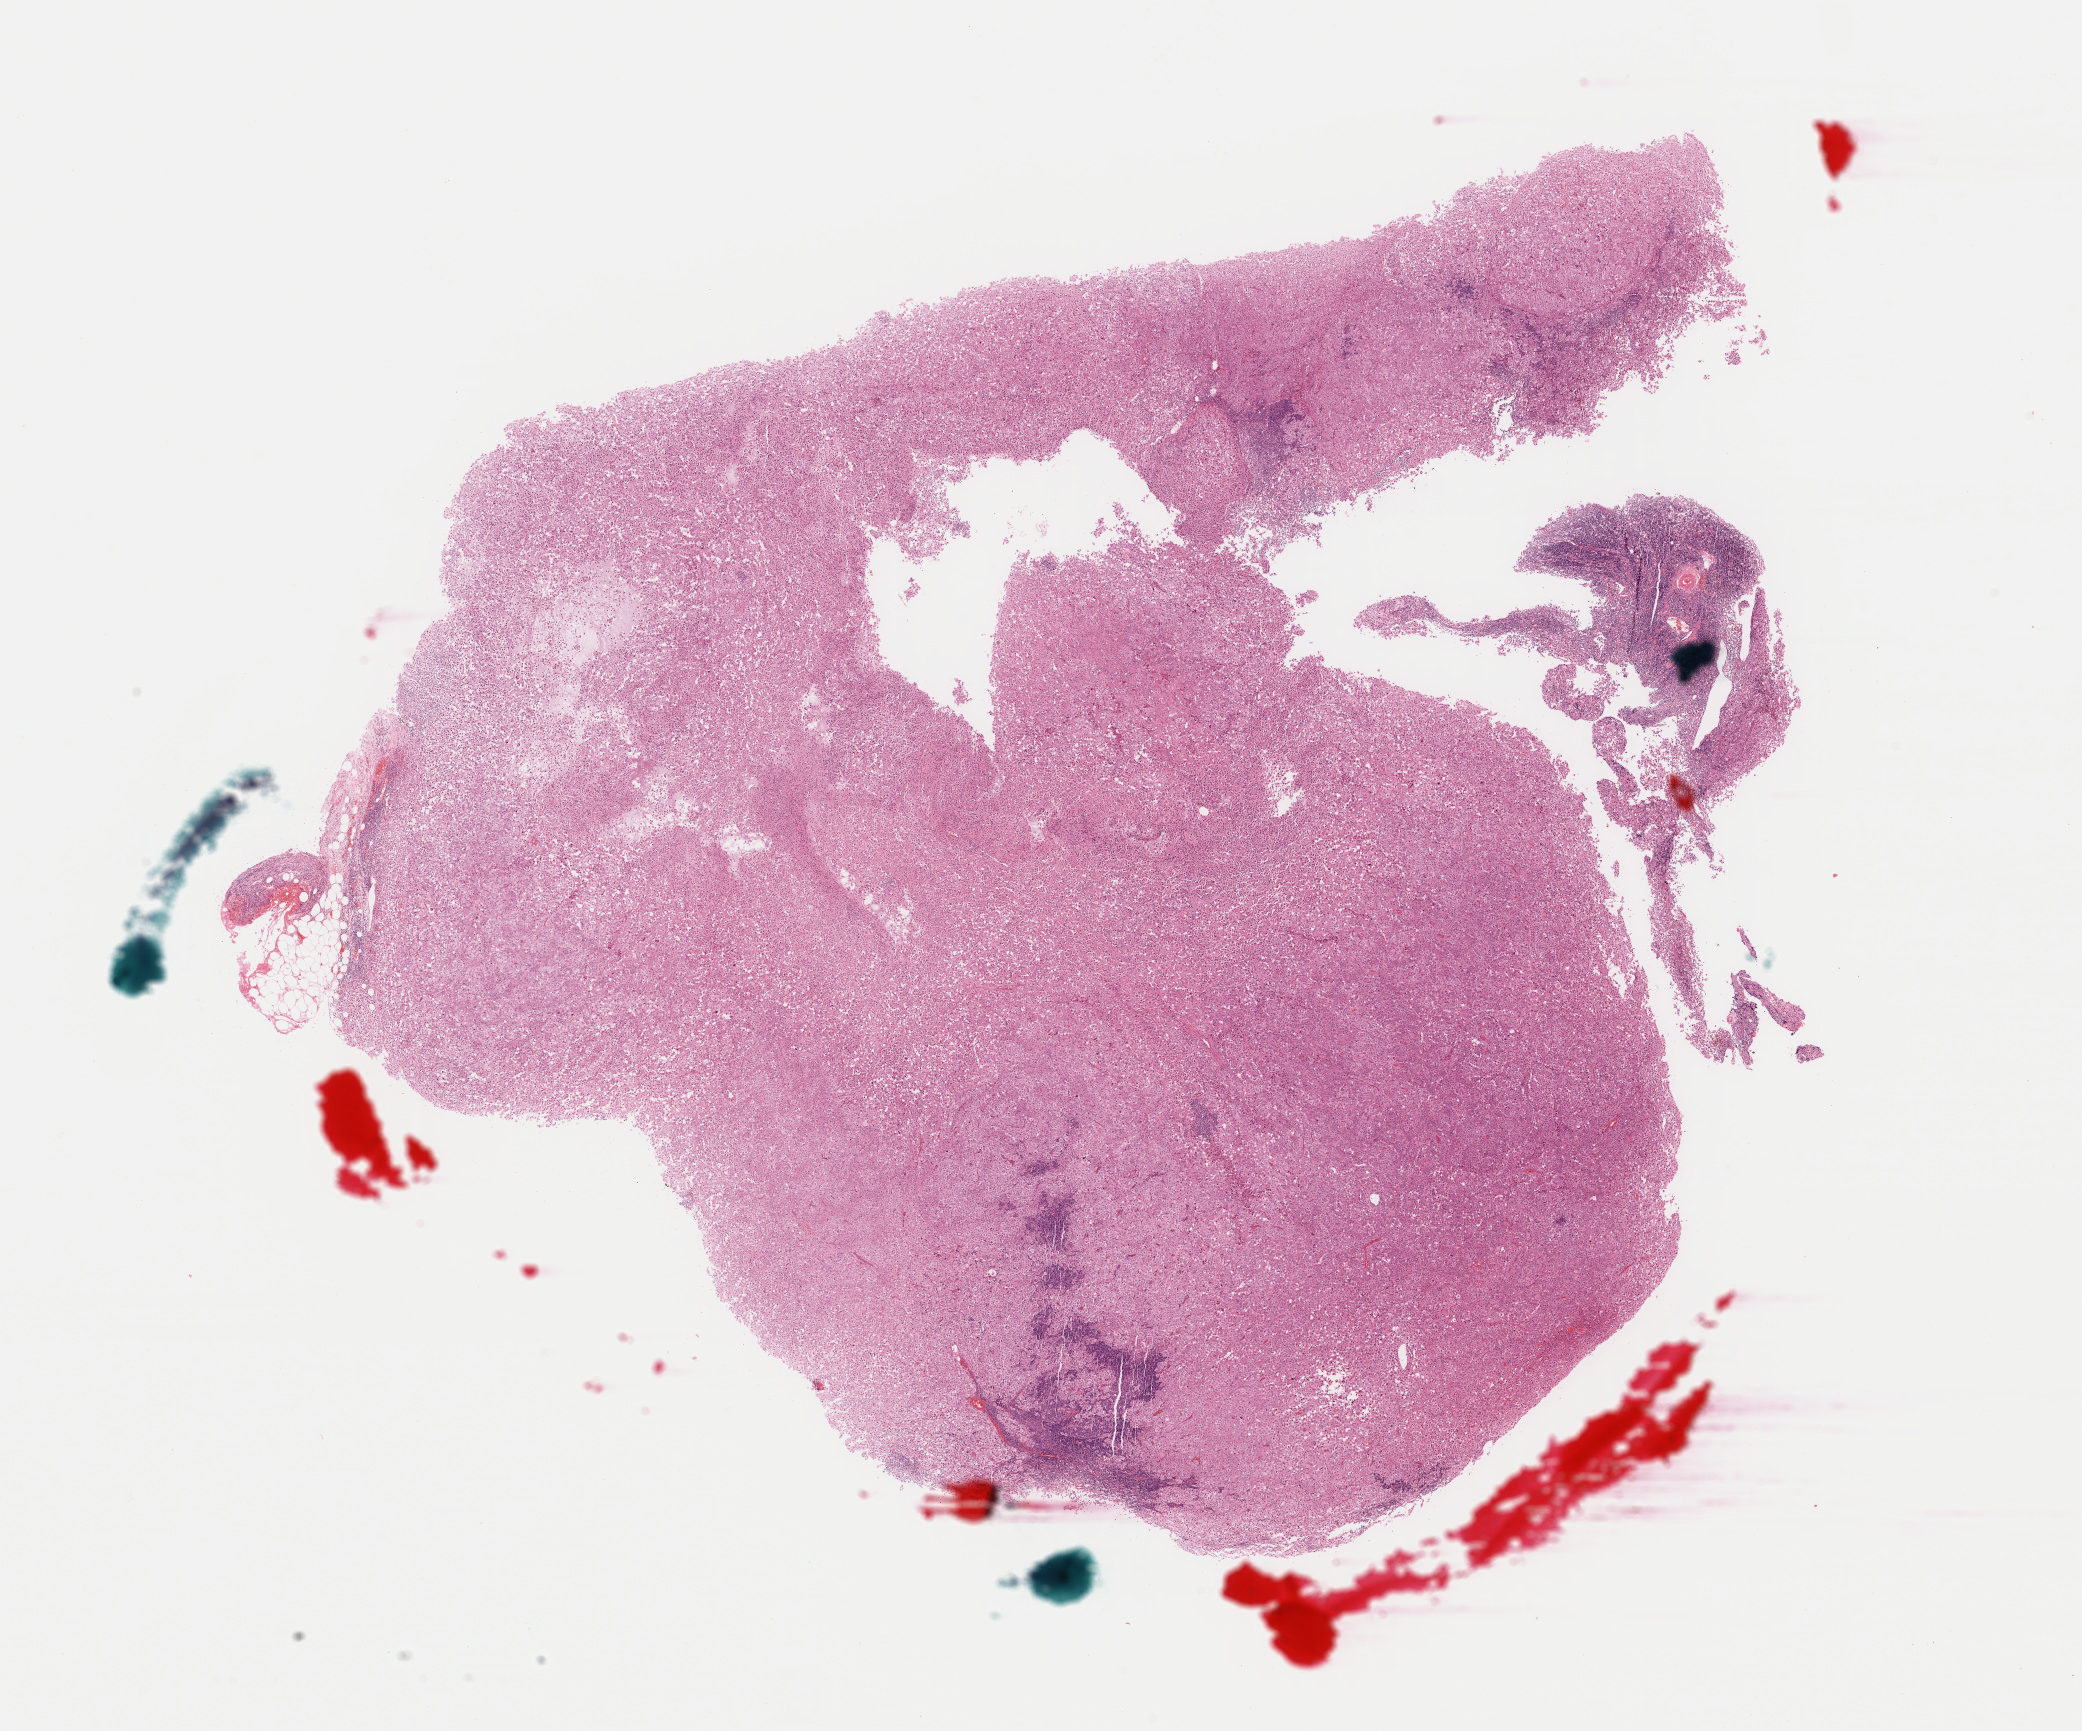
Digitized Hematoxylin and eosin (H&E) stained tissue section (whole slide), shown as a low-resolution overview of the whole scanned area (about 16.4 x 13.7 mm). Formalin-fixed paraffin-embedded (FFPE) diagnostic section. Metastatic tumour sample. Male patient; age at initial diagnosis 69 years.
This section: metastatic tumour tissue. Patient diagnosis: Malignant melanoma, NOS.